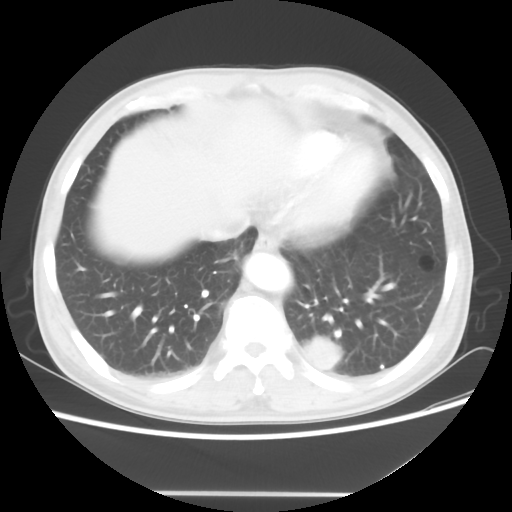
Chest CT, one axial slice. Slice 15 of 60 in the series (ordered by position). Reconstruction kernel STANDARD. 100 kVp. Lung window (W 1500 / L -600 HU). 5 mm slice thickness. 512 × 512 image matrix, field of view 360 × 360 mm. Male patient, age 55 years. Case-level facts recorded for this patient, not image findings: clinical TNM (as recorded): T1c N3 M0; histopathological grade: G3.
Structures marked on this image (bounding box drawn by a radiologist):
- lung tumour (recorded histology: small cell carcinoma): bounding box <303,336,343,380> (left, top, right, bottom; pixels)